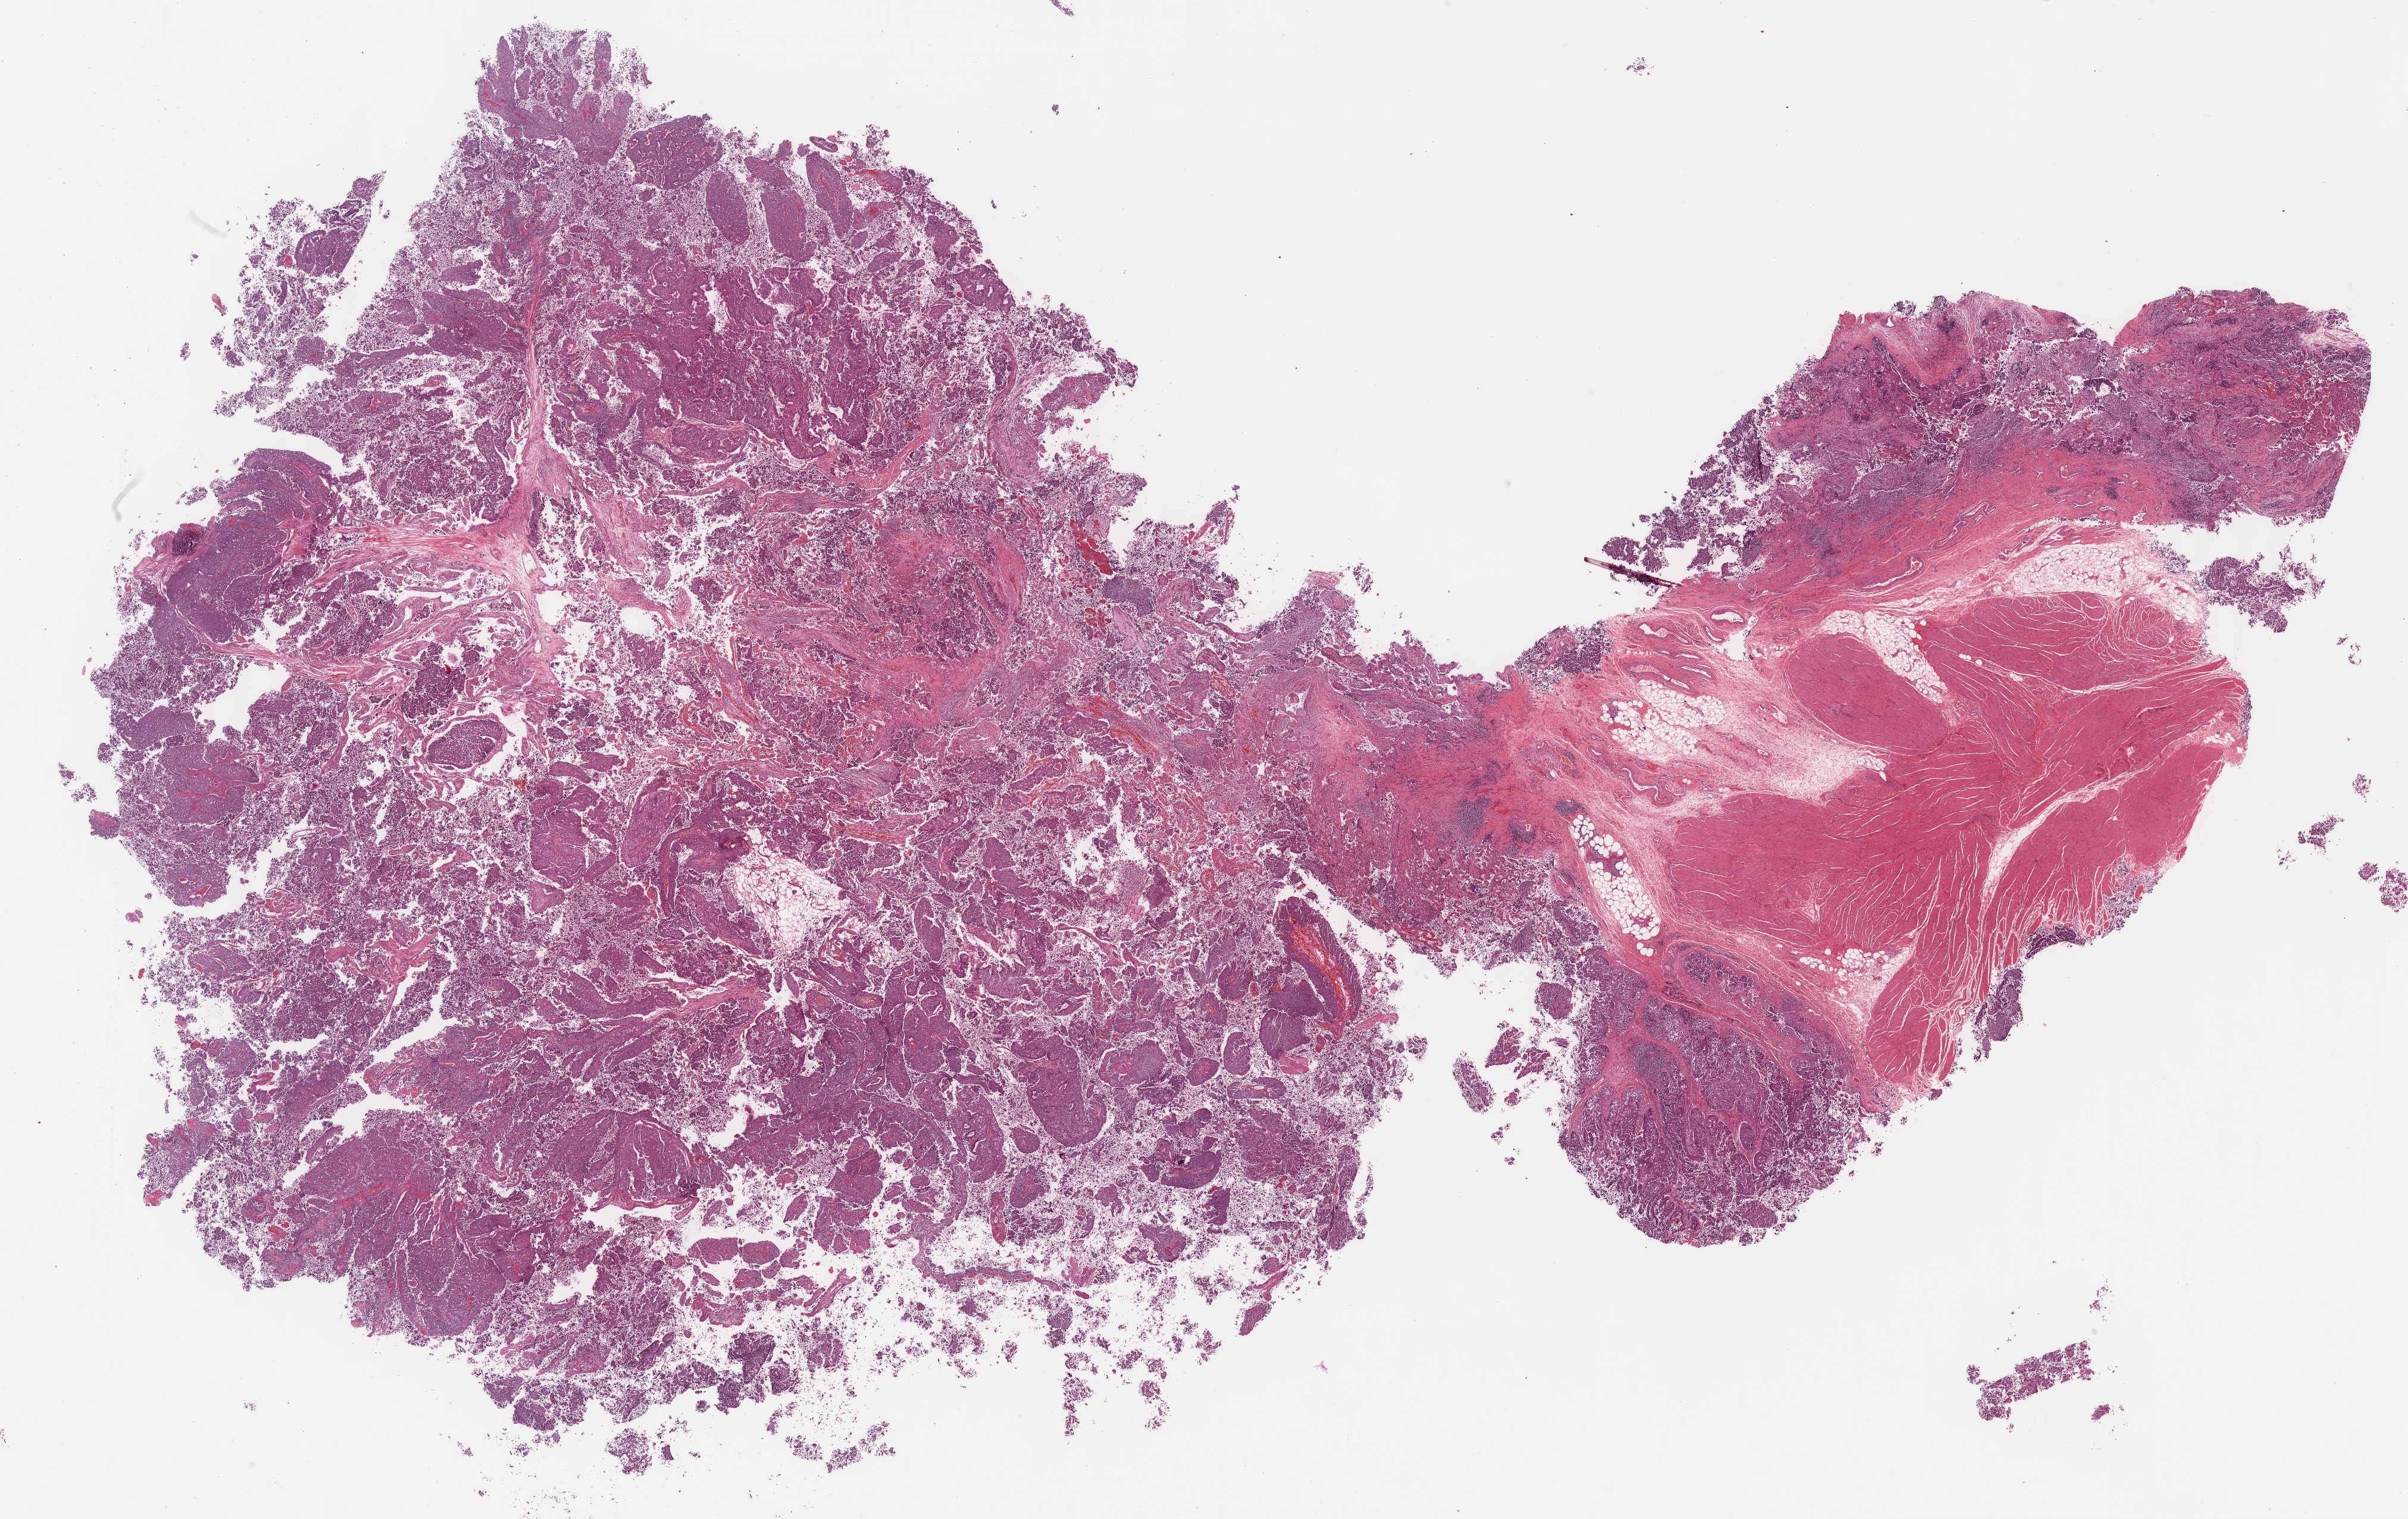
Digitized H&E tissue section (whole slide), a low-resolution overview of the entire scanned area, about 32.7 x 20.6 mm; formalin-fixed paraffin-embedded (FFPE) diagnostic section; sample: primary tumour, bladder. Patient: male, age at initial diagnosis 67 years.
Diagnosis: Transitional cell carcinoma (anterior wall of bladder).